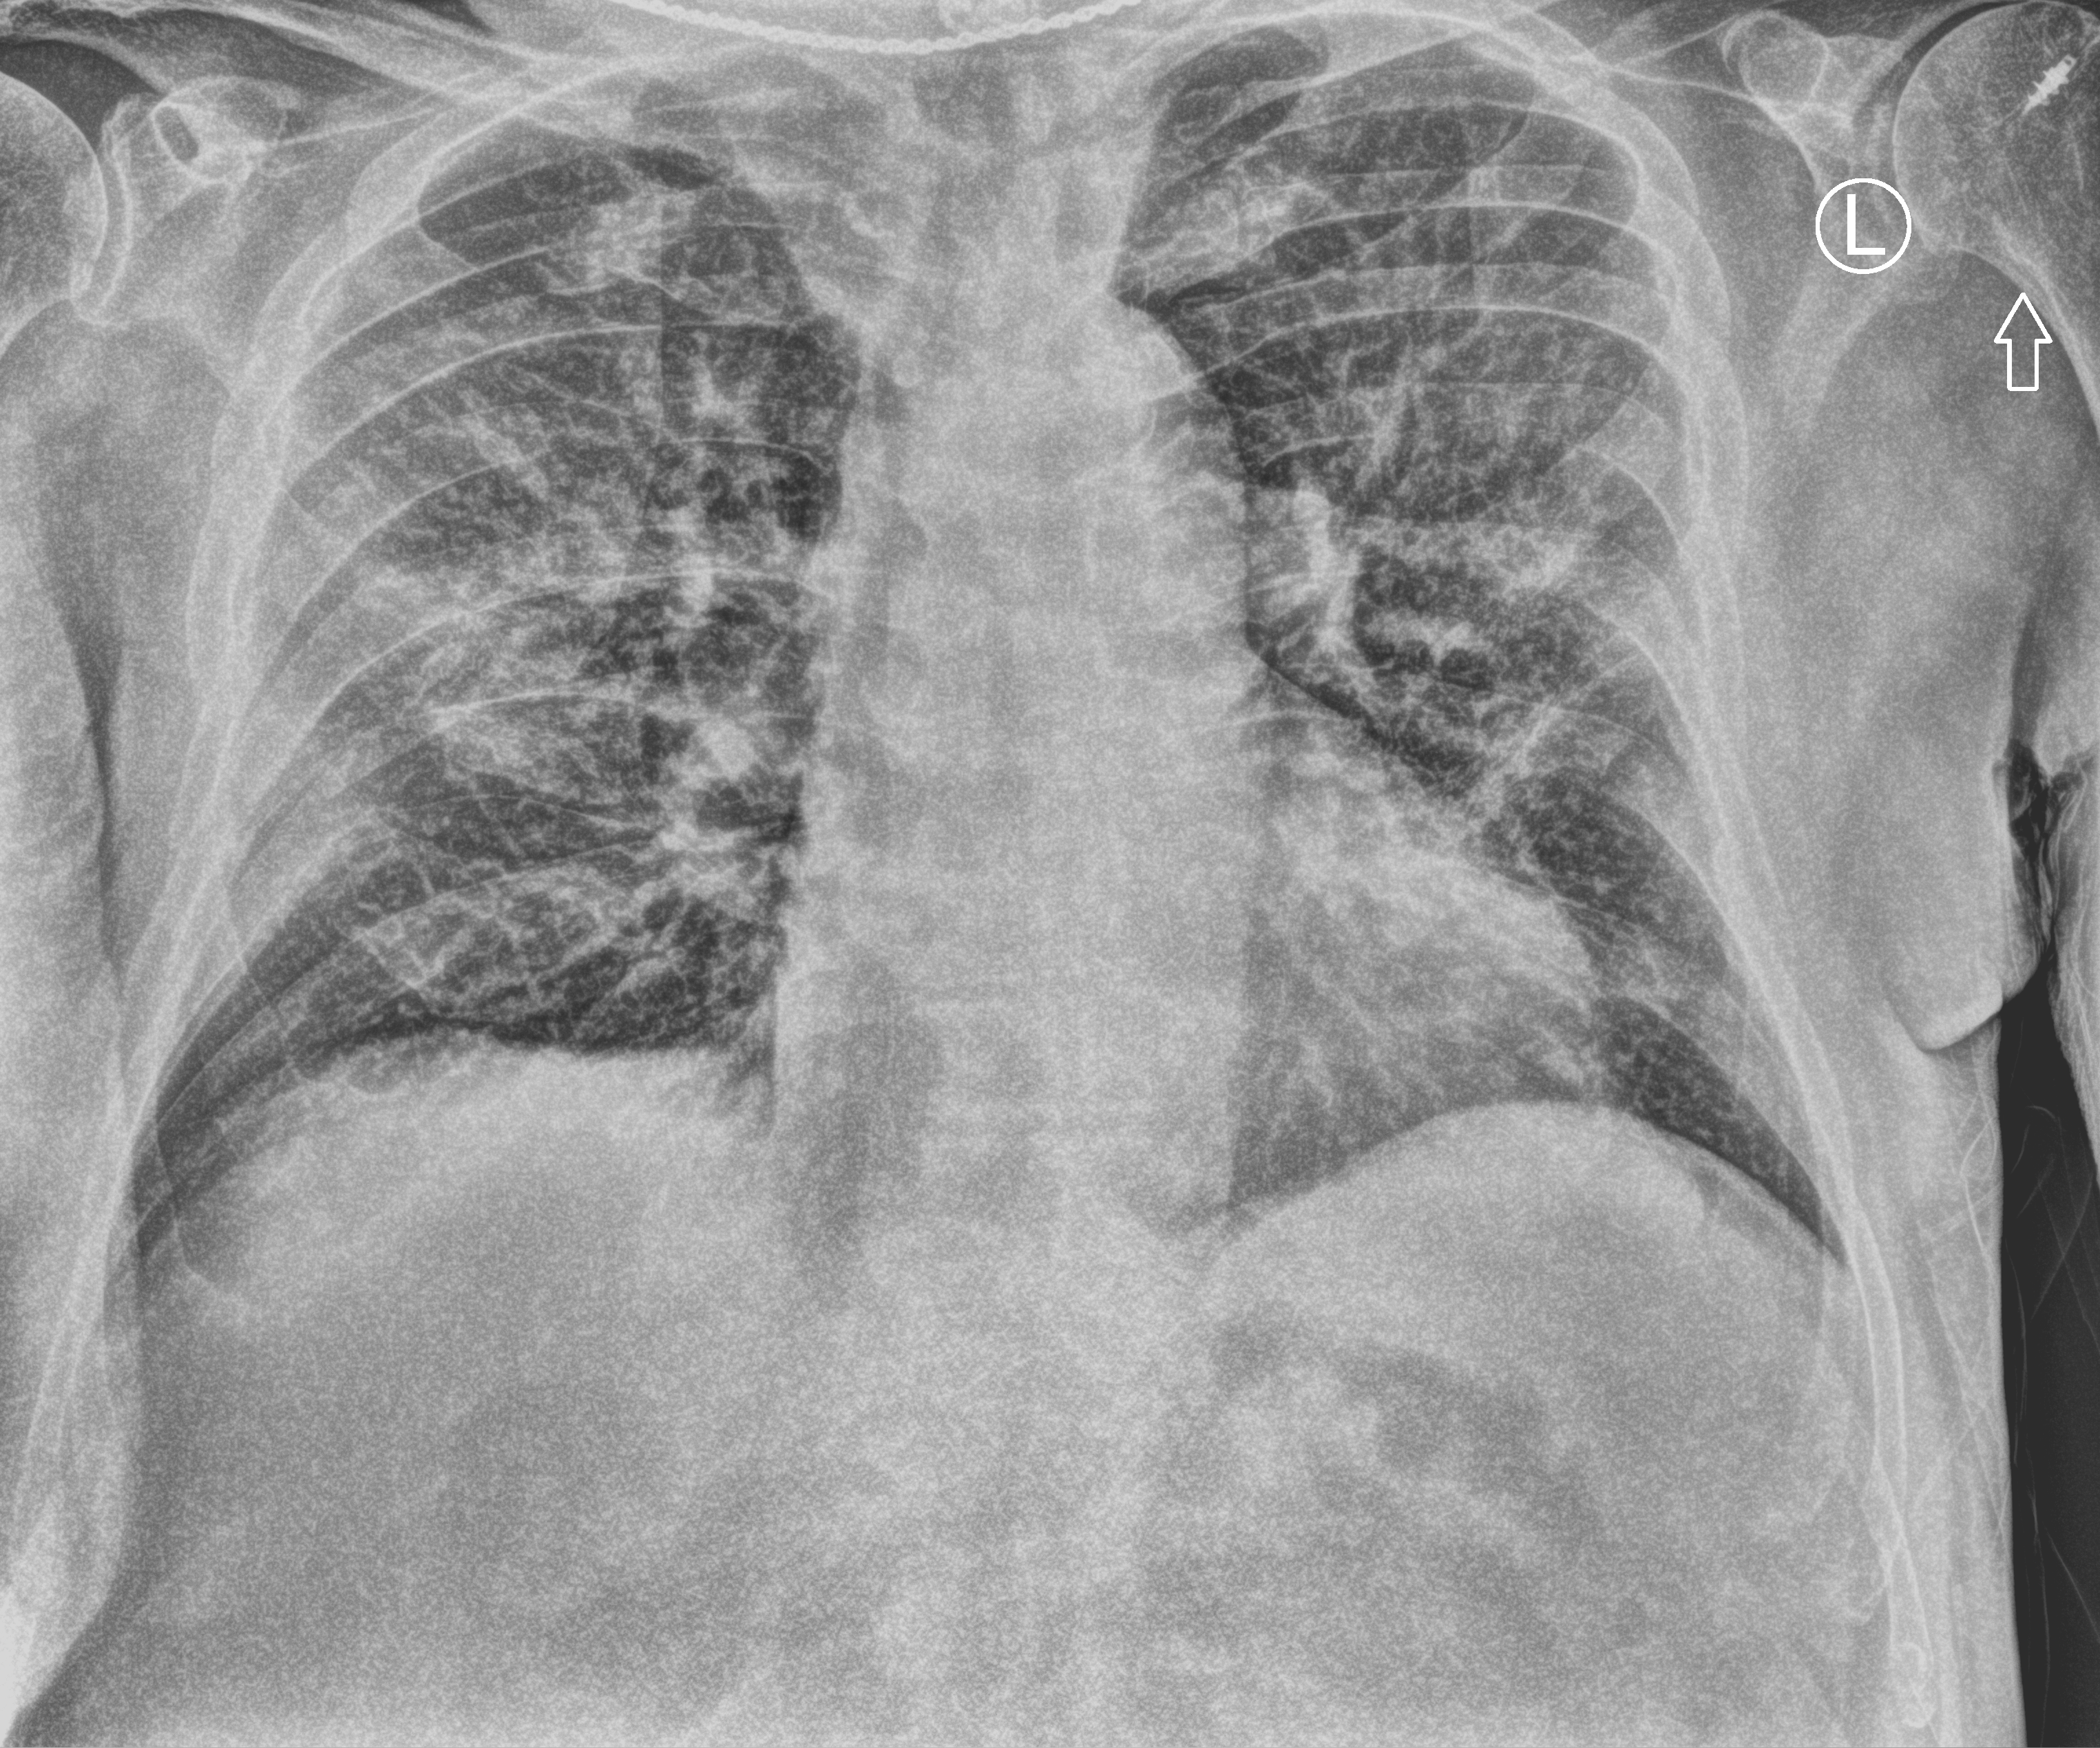
Bedside chest radiograph (computed radiography); anteroposterior (AP) projection. Patient hospitalised with COVID-19; male, aged 75–90 years.
Admission-level facts for this patient (not findings on this image; timing relative to this image not recorded):
- length of hospital stay: 26 days